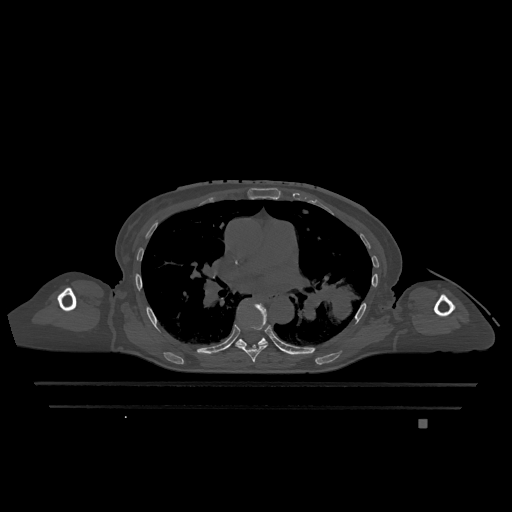
CT including the spine, one axial slice; position 768 of 1317 along the scan axis; bone window (W 1800 / L 400 HU); 0.5 mm slice thickness; 512 × 512 image matrix, field of view 500 × 500 mm. Female patient, age 74 years. From the clinical record (not read from this slice): primary cancer: lung; vertebrae with lytic lesions (as recorded): T1, T4, T5, T6, L4, L5.
Structures marked on this image (semi-automatically segmented with operator editing):
- T6 vertebra: bounding box (x1, y1, x2, y2) in pixels: (237, 303, 270, 362)
- T7 vertebra: (236, 337, 268, 346)